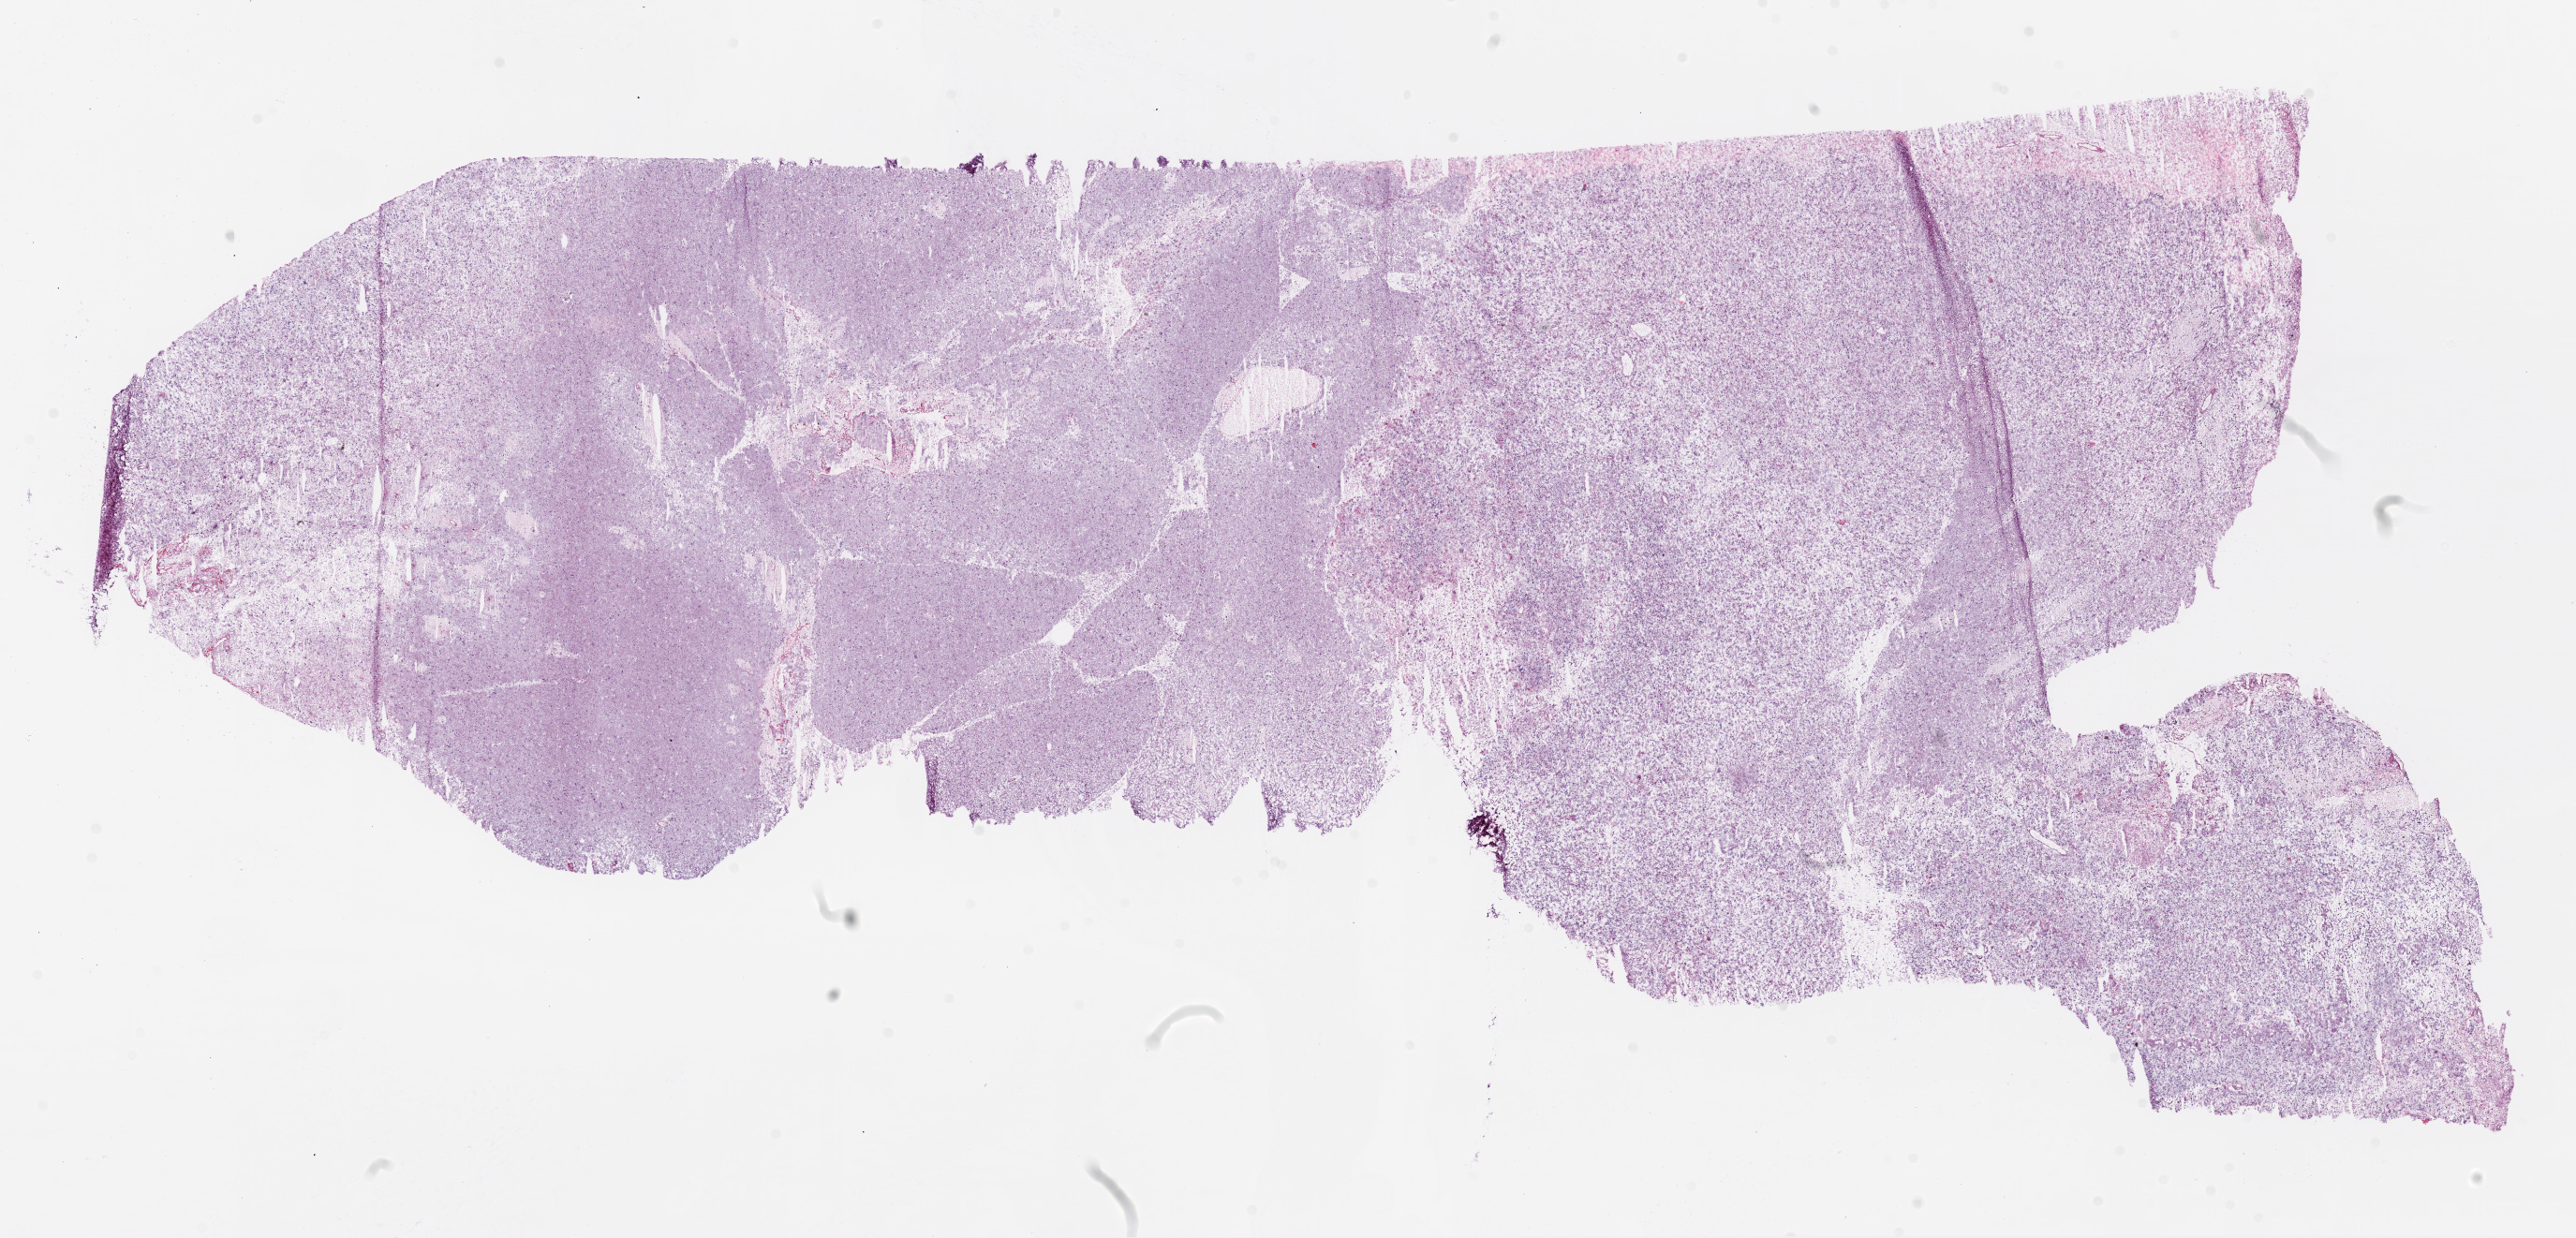
H&E whole-slide image — low-resolution overview of the scanned area, about 22.1 x 10.6 mm. Frozen section from the top of the tissue portion. Brain, primary tumour sample. Male, age 59 years at initial diagnosis. Pathologist review of this section (percent, as recorded): tumour cells 95%, tumour nuclei 80%, normal cells 0%, stromal cells 0%, necrosis 5%.
Diagnosis: Glioblastoma.